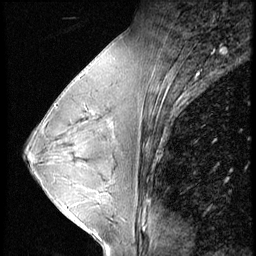
Breast MRI (dynamic contrast-enhanced), one sagittal slice. 4 images stored at this slice position (order not interpretable as contrast timing). 1.5 T. TE 4.2 ms, TR 9 ms. 2.5 mm slice thickness. 256 × 256 image matrix, field of view 180 × 180 mm. Female patient, age 45 years. Case-level facts recorded for this patient, not image findings: setting: breast cancer imaged before/during neoadjuvant chemotherapy; receptor status: triple-negative.
Structures marked on this image (semi-automatically segmented with operator editing):
- analysis volume of interest (the breast-tissue region the enhancement analysis was run in; not a lesion): bounding box (x1, y1, x2, y2) in pixels: (77, 104, 97, 124)
- tumour enhancement mask (voxels above the 140 % enhancement threshold inside the analysis volume of interest): (78, 104, 96, 124)